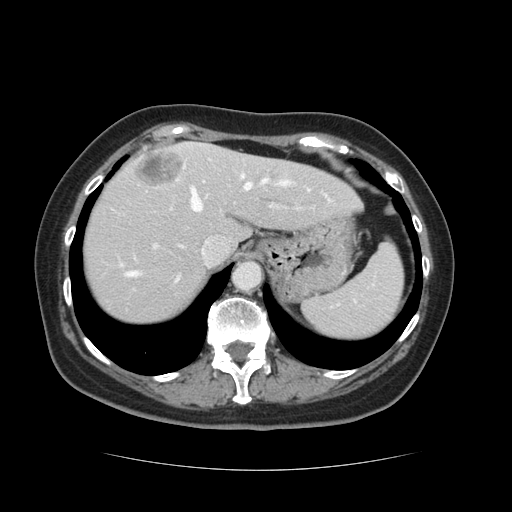
Contrast-enhanced abdominal CT, one axial slice; position 99 of 128 along the scan axis; 120 kVp; intravenous contrast given; soft-tissue window (W 400 / L 40 HU); 512 × 512 image matrix, field of view 366 × 366 mm. Female patient, age 67 years. From the clinical record (not read from this slice): diagnosis: colorectal cancer liver metastases, imaged before liver resection; multiple liver metastases: yes; largest metastasis: 3 cm; disease in both lobes: yes.
Structures marked on this image (manually delineated by an expert):
- hepatic veins: box from (x=126, y=174) to (x=293, y=283) px
- liver: (x=83, y=144)–(x=360, y=326)
- planned liver remnant (the part of the liver to remain after resection): (x=83, y=155)–(x=360, y=325)
- portal vein (with intrahepatic branches): (x=154, y=159)–(x=280, y=247)
- liver metastasis: (x=136, y=151)–(x=188, y=186)